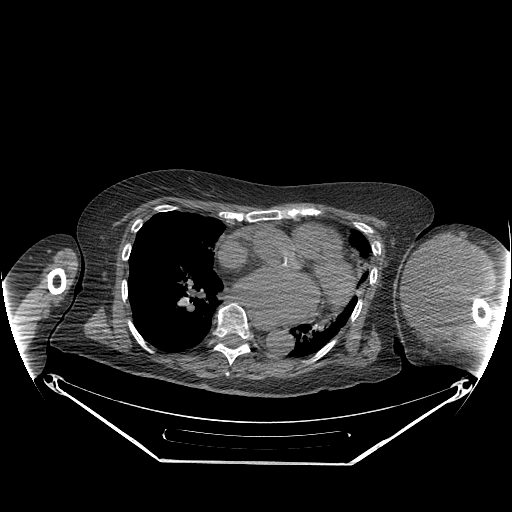
CT of an extremity soft-tissue mass (from a PET/CT study), one axial slice. Position 166 of 267 along the scan axis. Reconstruction kernel STANDARD. 140 kVp. Soft-tissue window (W 400 / L 40 HU). 3.75 mm slice thickness. 512 × 512 image matrix. Female patient. From the clinical record (not read from this slice): histological type: pleiomorphic leiomyosarcoma; grade: high; site of the primary tumour: left biceps.
Outlined on this slice (expert contour drawn on MRI and transferred to this co-registered scan by the dataset authors):
- gross tumour volume including surrounding oedema: bounding box (x1, y1, x2, y2) in pixels: (402, 235, 489, 330)
- gross tumour volume (mass): (402, 235, 483, 328)